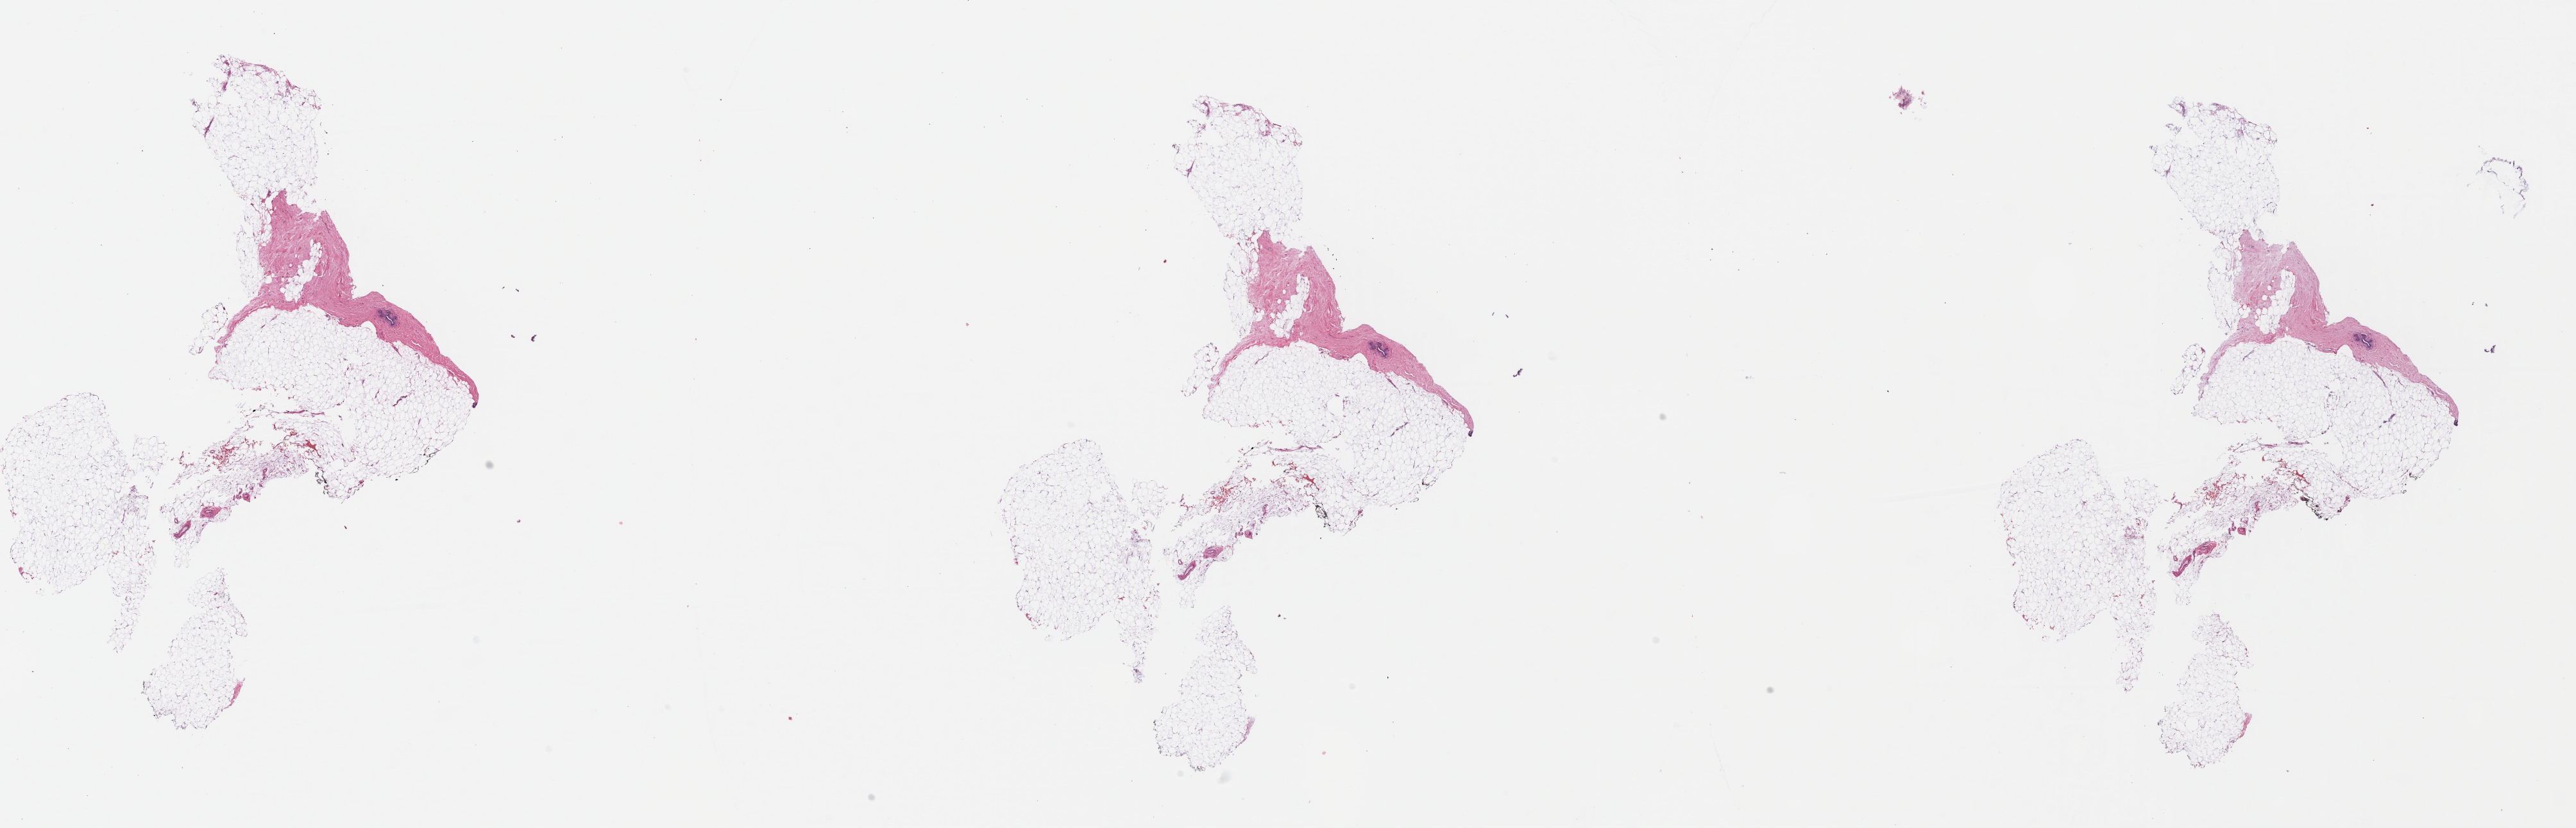
H&E-stained whole-slide image, whole scanned area (about 31.6 x 10.1 mm, slide scanned at 40x) shown as a low-resolution overview; formalin-fixed paraffin-embedded (FFPE) diagnostic section; sample: primary tumour, breast. Female, age 48 years at initial diagnosis.
AJCC pathologic stage: IIIC (7th edition). Diagnosis: Lobular carcinoma, NOS. Lymph nodes positive (case pathology): 21 of 24 examined. TNM: T2 N3a M0.